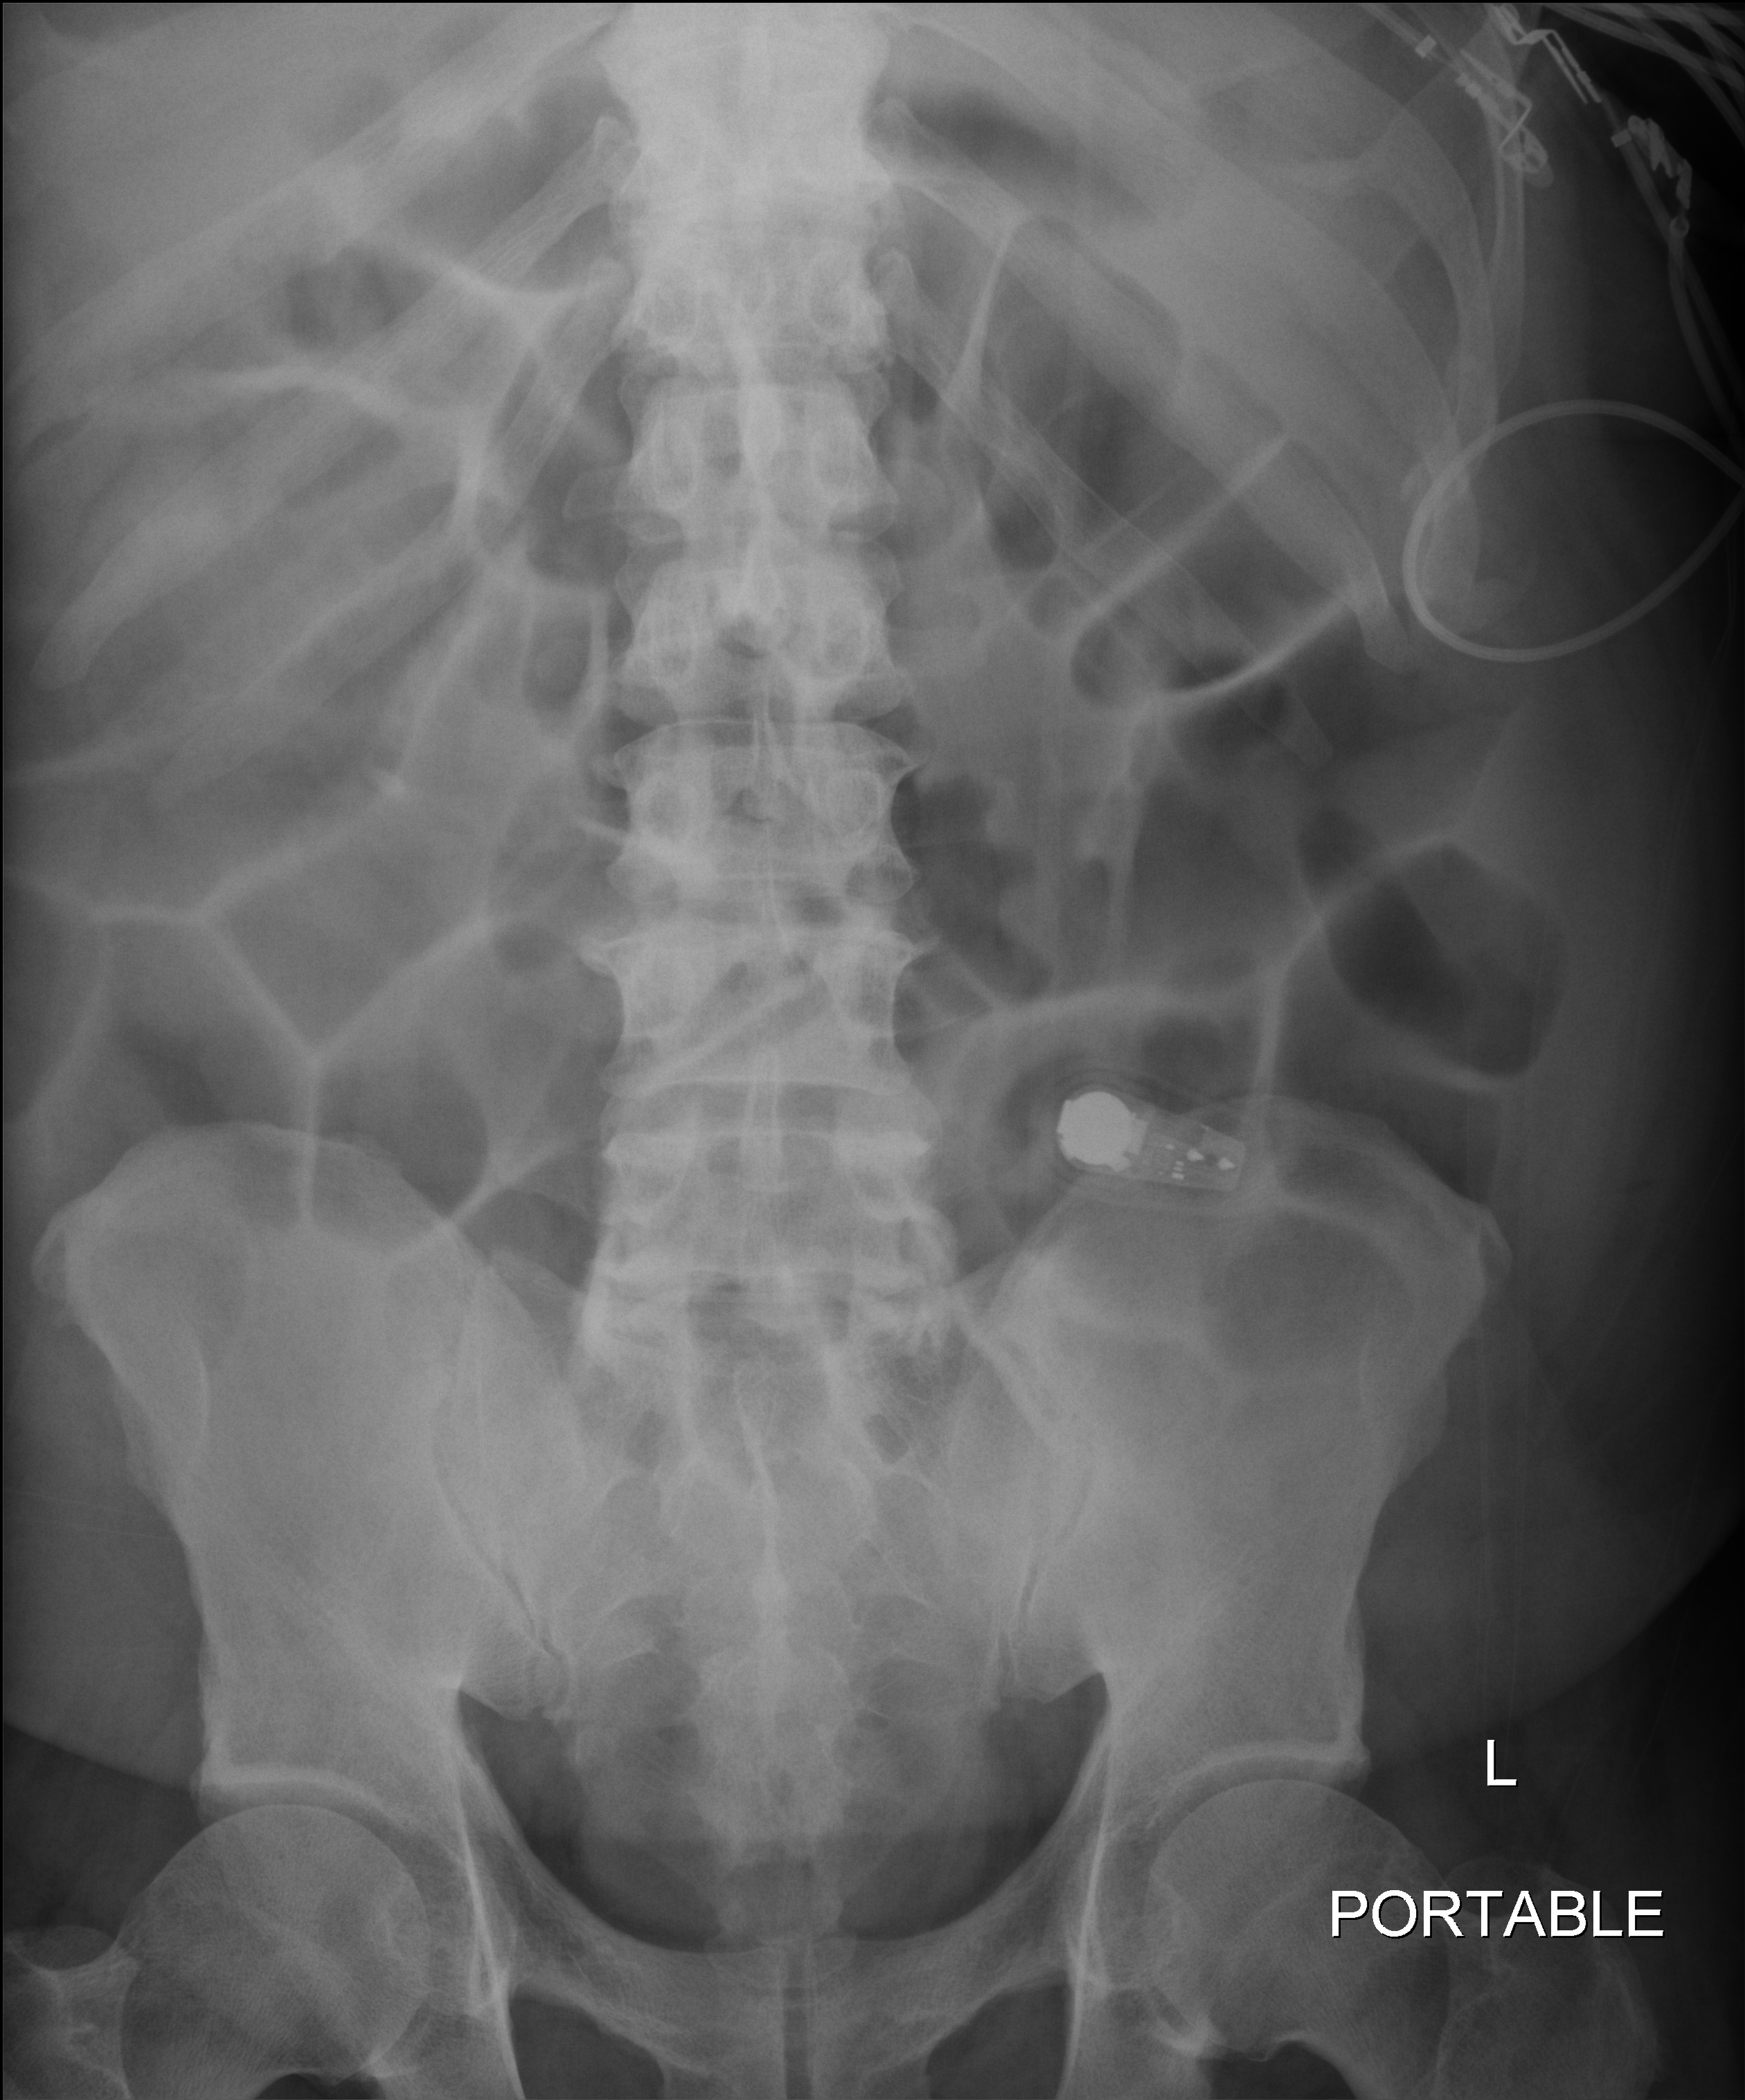
Portable abdomen radiograph; anteroposterior (AP) projection. Male patient hospitalised with COVID-19, age 18–59 years.
Hospital-stay facts (about this admission, not read from this image; timing relative to this image not recorded):
- diabetes (admission record): no